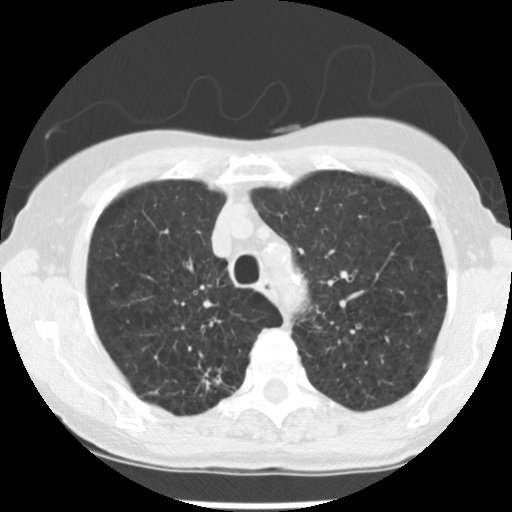
Axial slice from a low-dose chest CT screening exam; baseline screening round; lung window (W 1500 / L -600 HU); 2.5 mm slice thickness. Female, age 72 years at enrolment.
Expert-annotated lung lesion, bounding box [x1, y1, x2, y2] px = [183, 351, 240, 406]. The screening reader recorded 3 non-calcified nodules or masses ≥4 mm on this exam (right upper lobe, left upper lobe, left lower lobe); which of them this box marks is not recorded. Official screen result: positive, change unspecified: nodule(s) >= 4 mm or enlarging nodule(s), mass(es), or other non-specific abnormalities suspicious for lung cancer.